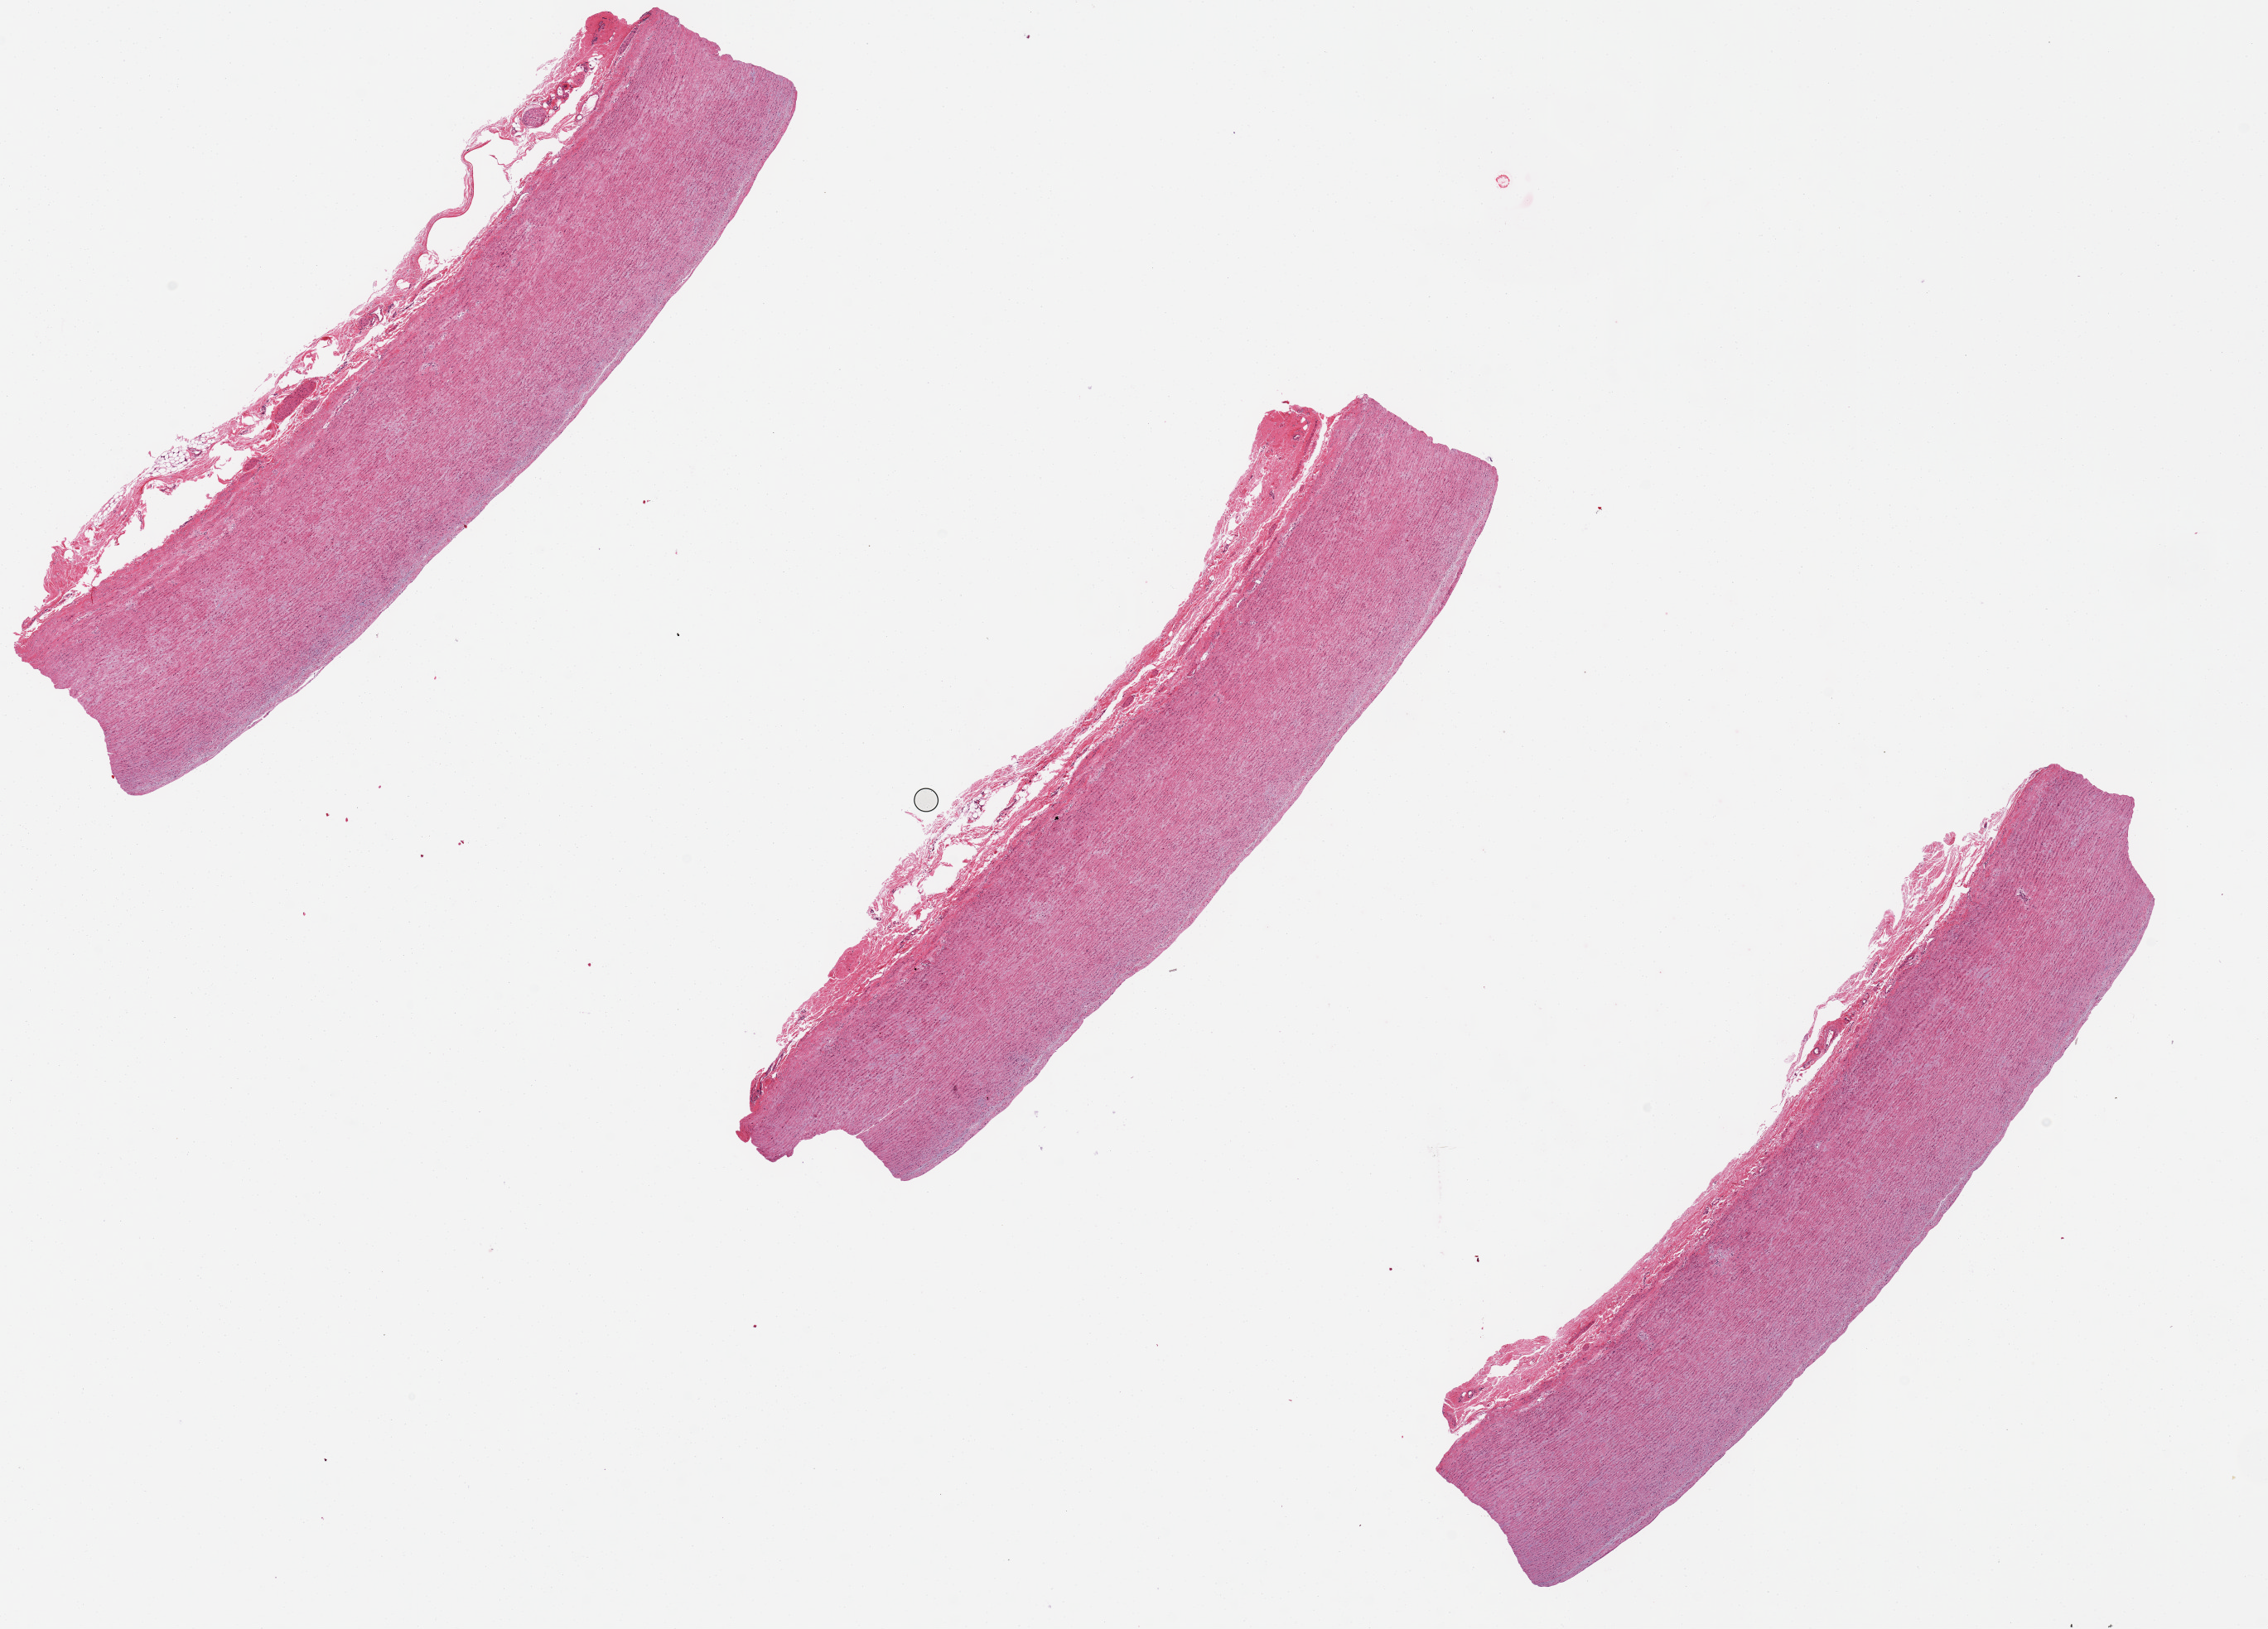
Whole-slide image, H&E stain — a low-resolution overview of the entire scanned area, about 21.7 x 15.6 mm (acquisition: 20x scan). PAXgene-fixed paraffin-embedded (PFPE) section. Section of aorta (target tissue). Donor tissue sample. Donor sex: female.
- reviewer comment on this tissue sample: No lesions